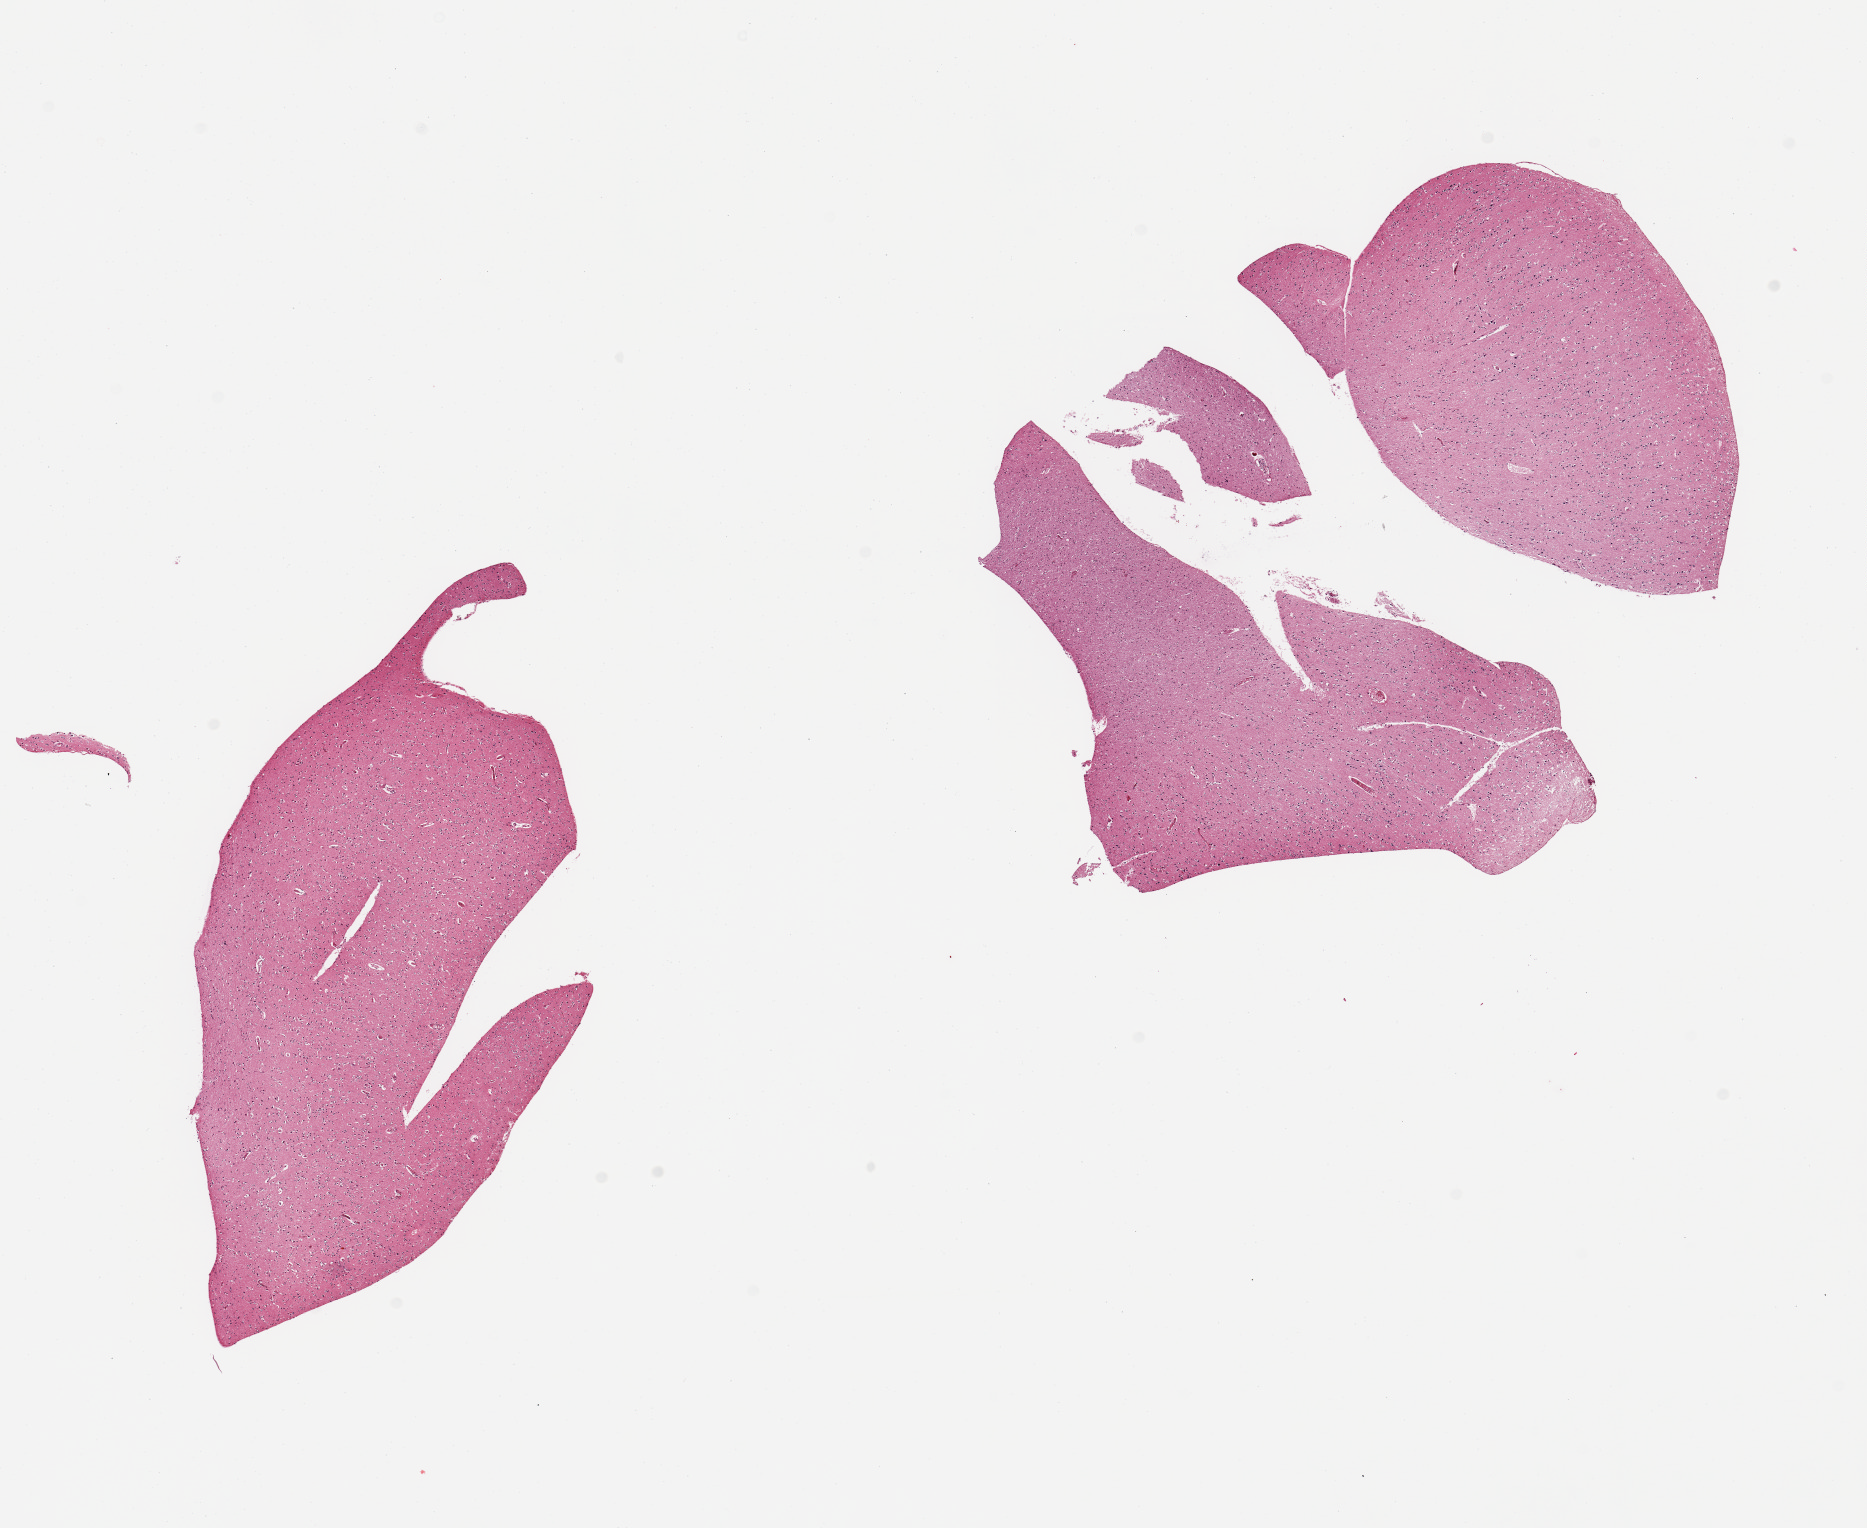
Hematoxylin and eosin (H&E) whole-slide image — whole scanned area (about 14.8 x 12.1 mm) shown as a low-resolution overview, PAXgene-fixed, paraffin-embedded tissue, sampled site (target tissue): cerebral cortex, tissue donor sample. Female donor.
Reviewer comment on this tissue sample: 3 pieces (fragmented).